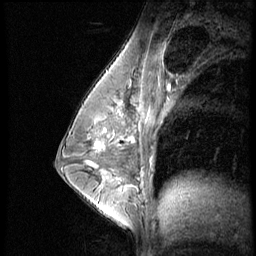
Breast MRI (dynamic contrast-enhanced), one sagittal slice; slice 34 of 56 in the series (ordered by position); dynamic contrast-enhanced series, image 2 of 4 at this slice position (ordered by acquisition); 1.5 T; TE 4.2 ms, TR 8.9 ms; 2.5 mm slice thickness; 256 × 256 image matrix. Patient: female, 35 years. From the clinical record (not read from this slice): setting: breast cancer imaged before/during neoadjuvant chemotherapy; receptor status: HER2-positive.
Structures marked on this image (semi-automatically segmented with operator editing):
- analysis volume of interest (the breast-tissue region the enhancement analysis was run in; not a lesion): bounding box (x1, y1, x2, y2) in pixels: (73, 111, 131, 164)
- tumour enhancement mask (voxels above the 140 % enhancement threshold inside the analysis volume of interest): (97, 138, 126, 146)